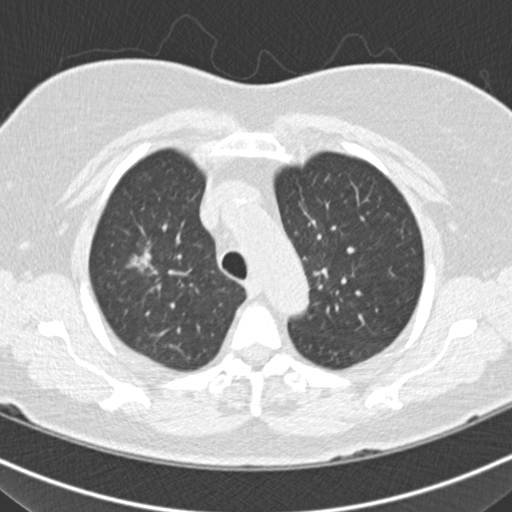
Low-dose screening chest CT, one axial slice. Position 134 of 160 along the scan axis. Reconstruction kernel B30f. 120 kVp. Lung window (W 1500 / L -600 HU). 2 mm slice thickness. 512 × 512 image matrix, field of view 316 × 316 mm.
Annotated regions visible in this slice (expert manual segmentation):
- lesion 3 (nodule, upper lobe of right lung): bounding box <132,251,151,271> (left, top, right, bottom; pixels)